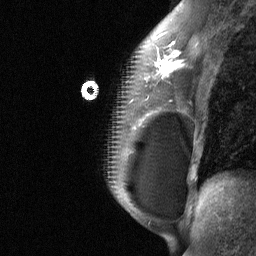
Breast MRI (dynamic contrast-enhanced), one sagittal slice; dynamic contrast-enhanced study with each time point stored as its own series, time point 2 of 3 at this slice position (early post-contrast, ordered by acquisition time); 1.5 T; TE 4.8 ms, TR 27 ms; 2 mm slice thickness; 256 × 256 image matrix, field of view 200 × 200 mm. Female patient, age 34 years. Case-level facts recorded for this patient, not image findings: setting: breast cancer imaged before/during neoadjuvant chemotherapy; receptor status: HR-positive, HER2-negative.
Structures marked on this image (semi-automatically segmented with operator editing):
- analysis volume of interest (the breast-tissue region the enhancement analysis was run in; not a lesion): box from (x=92, y=50) to (x=188, y=185) px
- tumour enhancement mask (voxels above the 90 % enhancement threshold inside the analysis volume of interest): (x=155, y=54)–(x=182, y=77)